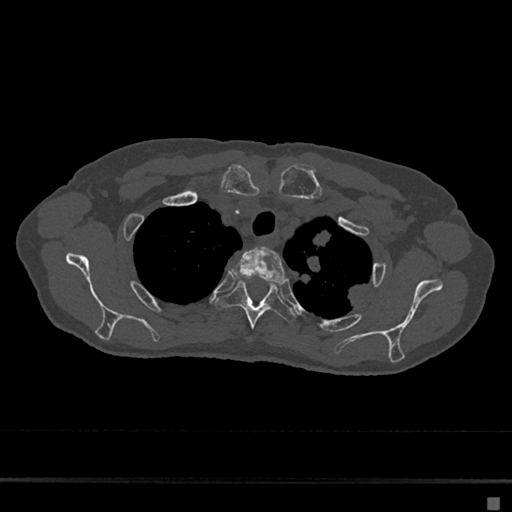
CT including the spine, one axial slice. Position 552 of 797 along the scan axis. Bone window (W 1800 / L 400 HU). 0.5 mm slice thickness. 512 × 512 image matrix, field of view 360 × 360 mm. Patient: female, 68 years. Case-level facts recorded for this patient, not image findings: primary cancer: renal.
Outlined on this slice (semi-automatically segmented with operator editing):
- T2 vertebra: bounding box [x1, y1, x2, y2] px = [232, 247, 287, 283]
- T3 vertebra: [216, 281, 296, 329]